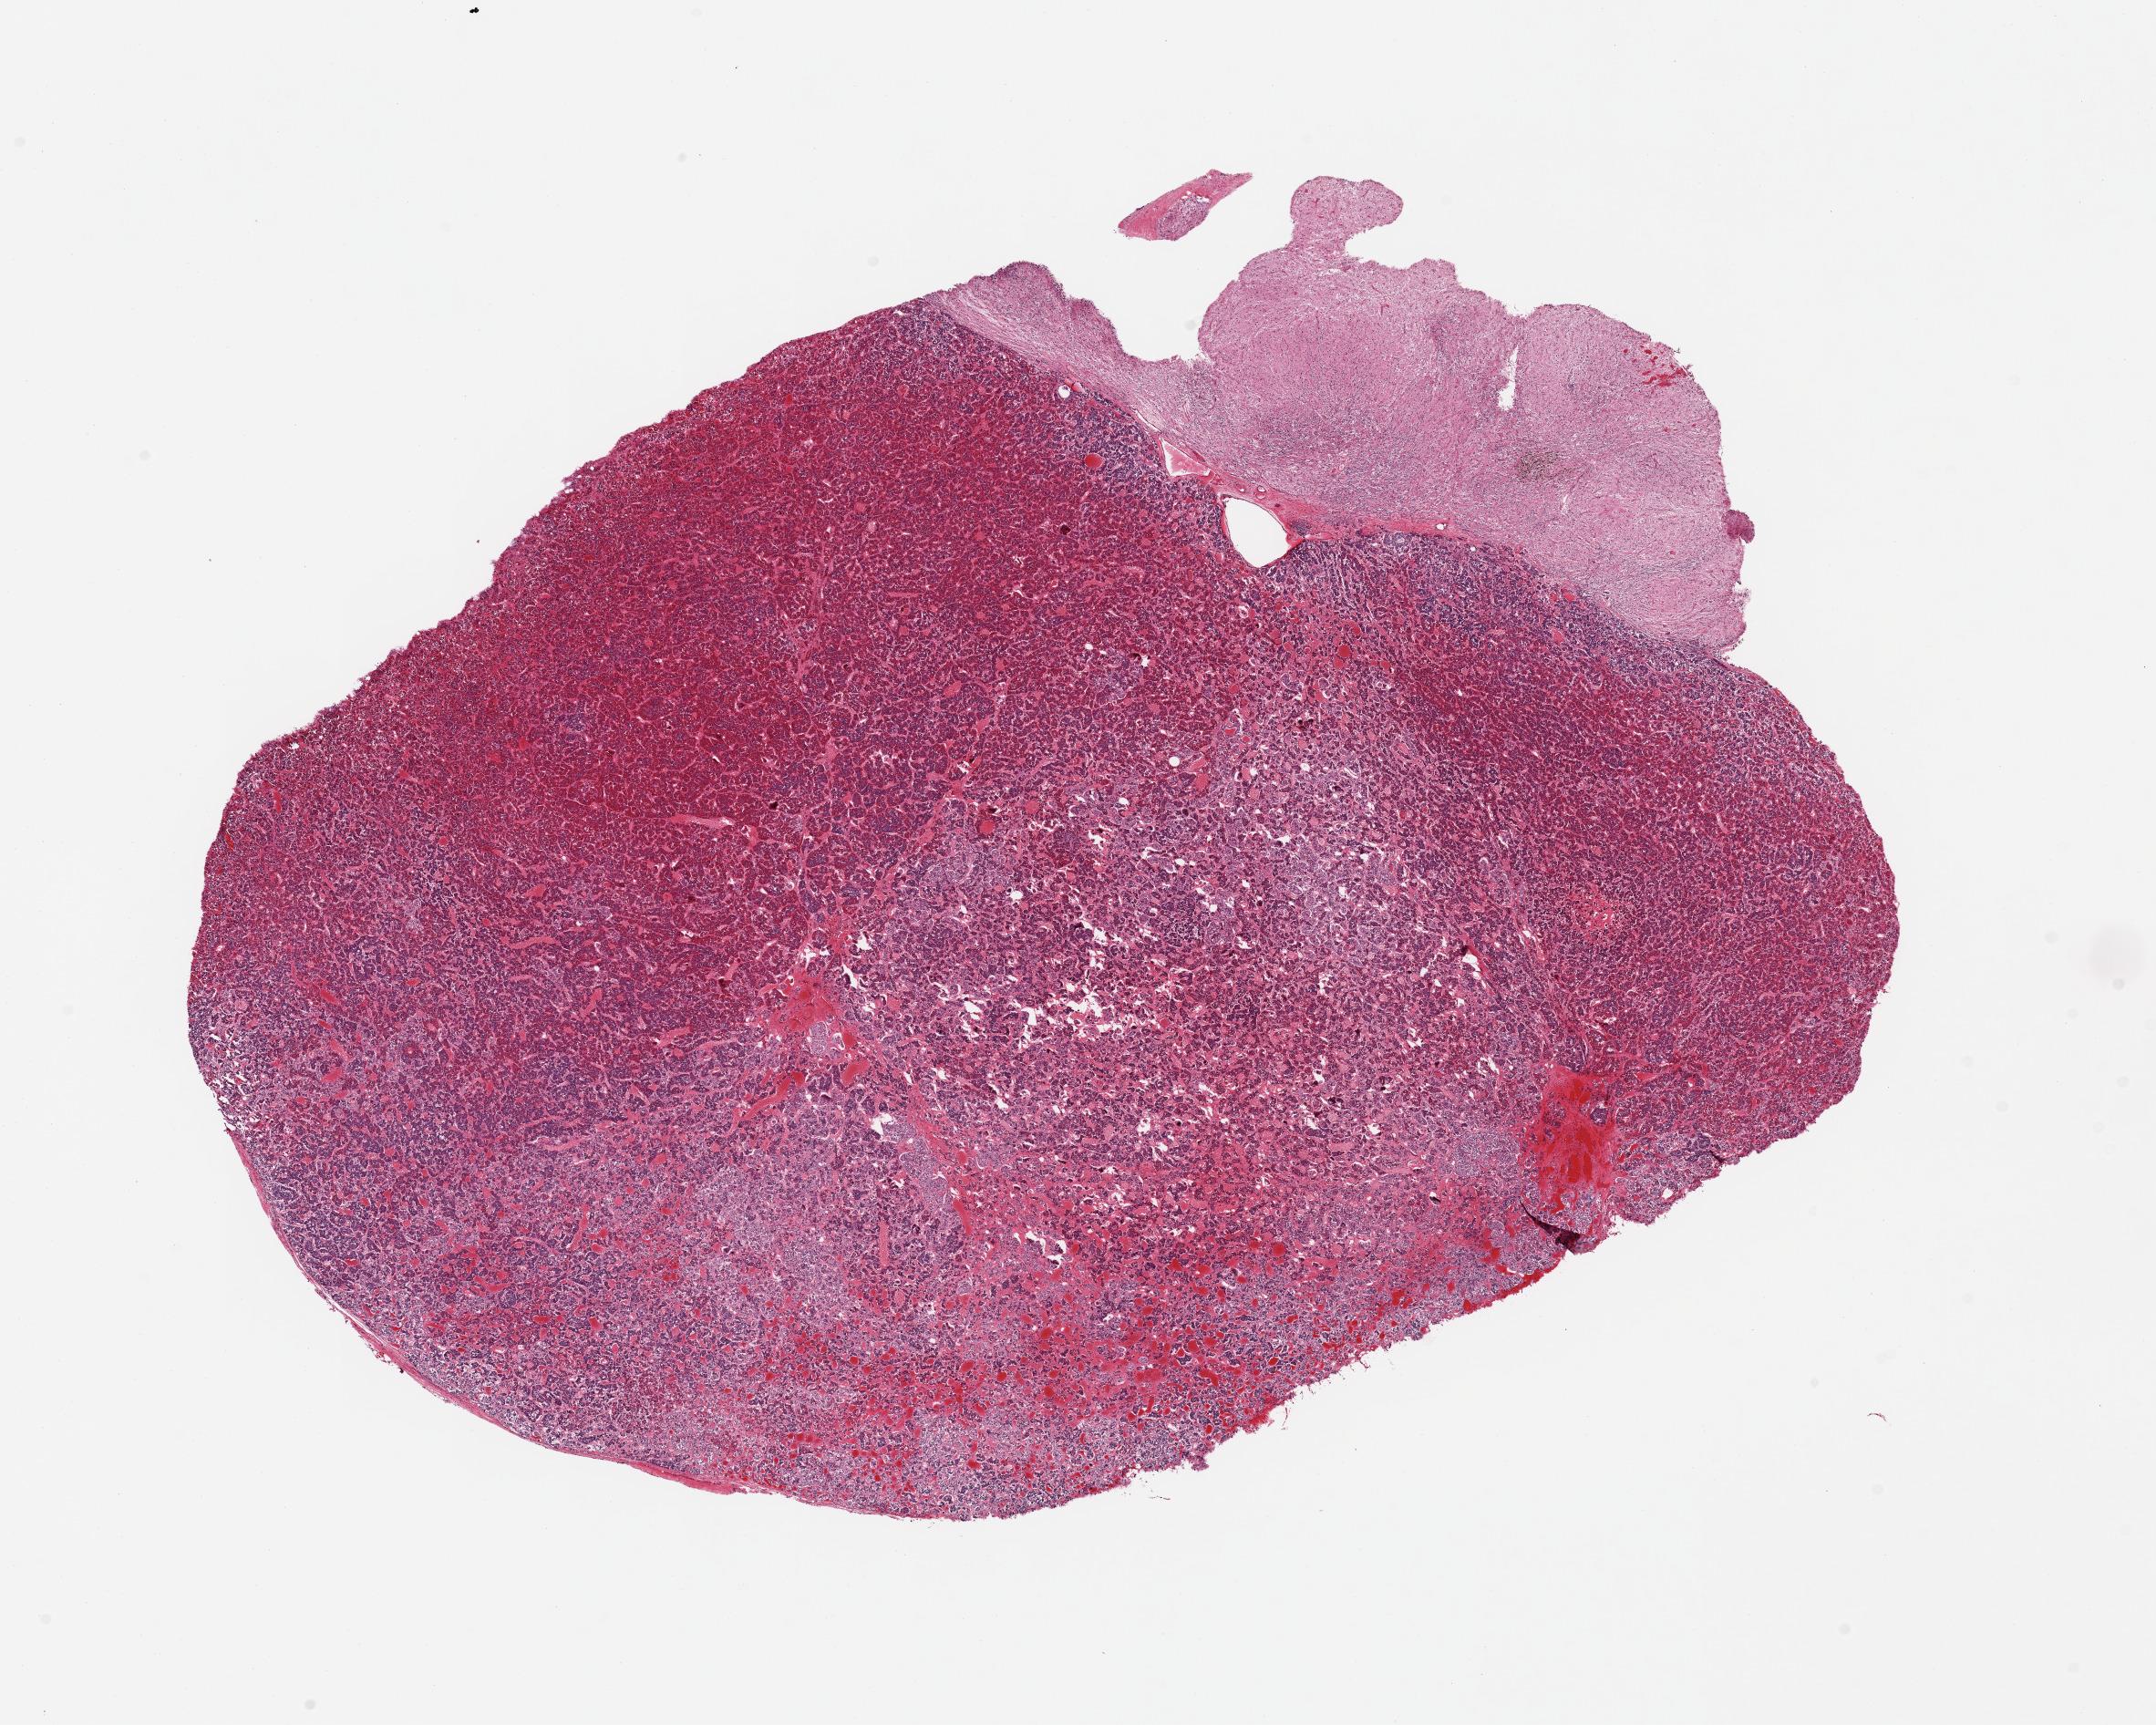
Digitized hematoxylin and eosin (H&E)-stained section, brightfield, whole scanned area (about 18.7 x 15.0 mm, acquisition: 20x scan) shown as a low-resolution overview. PAXgene-fixed paraffin-embedded (PFPE) section. Target tissue: pituitary. Donor tissue sample. Donor: female.
Review note (as recorded): 1 piece; 75% anterior; 25% posterior.